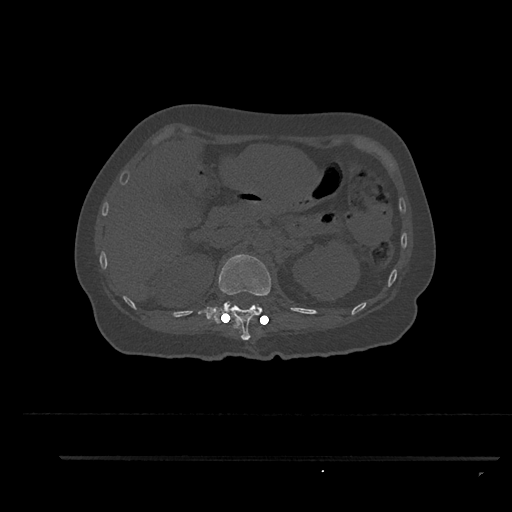
CT including the spine, one axial slice. Slice 247 of 797 in the series (ordered by position). 120 kVp. Bone window (W 1800 / L 400 HU). 0.5 mm slice thickness. 512 × 512 image matrix, field of view 408 × 408 mm. Female patient, age 44 years. From the clinical record (not read from this slice): primary cancer: renal.
Annotated regions visible in this slice (semi-automatically segmented with operator editing):
- L1 vertebra: bounding box <224,301,229,308> (left, top, right, bottom; pixels)
- T12 vertebra: <198,254,271,340>